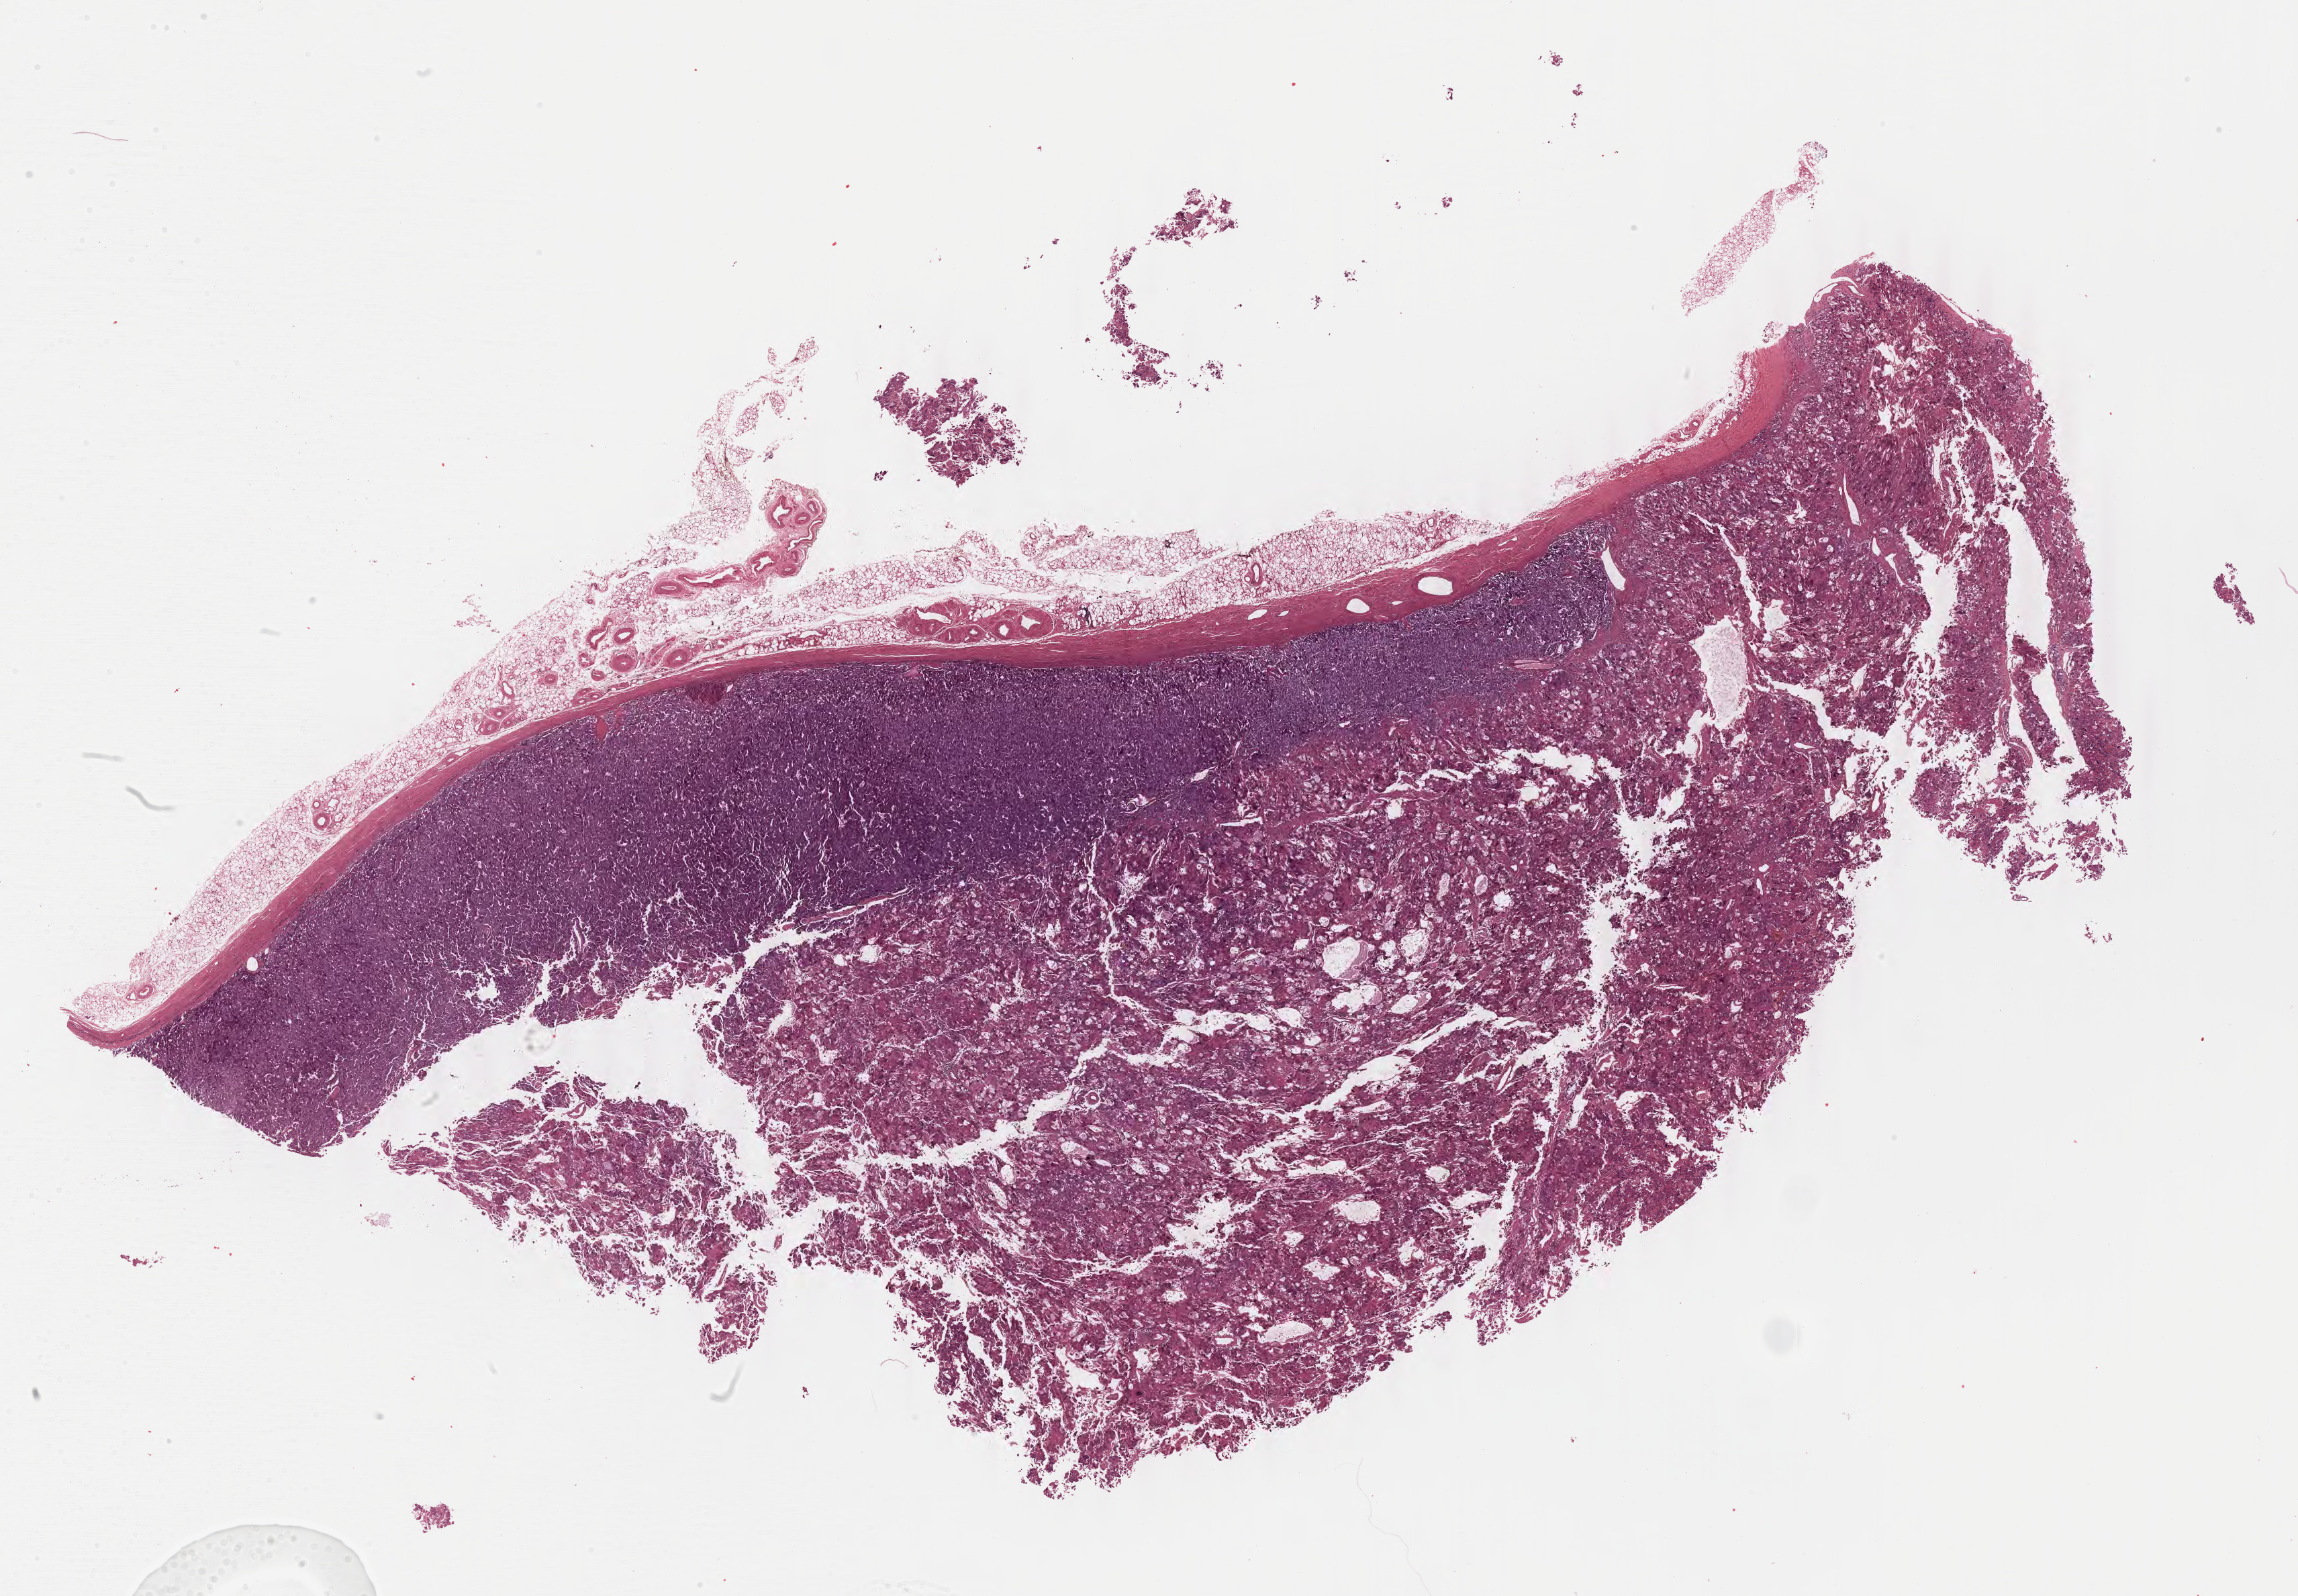
Whole-slide histology image, H&E-stained, a low-resolution overview of the entire scanned area, about 27.0 x 18.8 mm (acquisition: 40x scan), FFPE section, adrenal gland, primary tumour sample. Female patient; age at initial diagnosis 46 years.
Pathologic diagnosis: Pheochromocytoma, NOS.